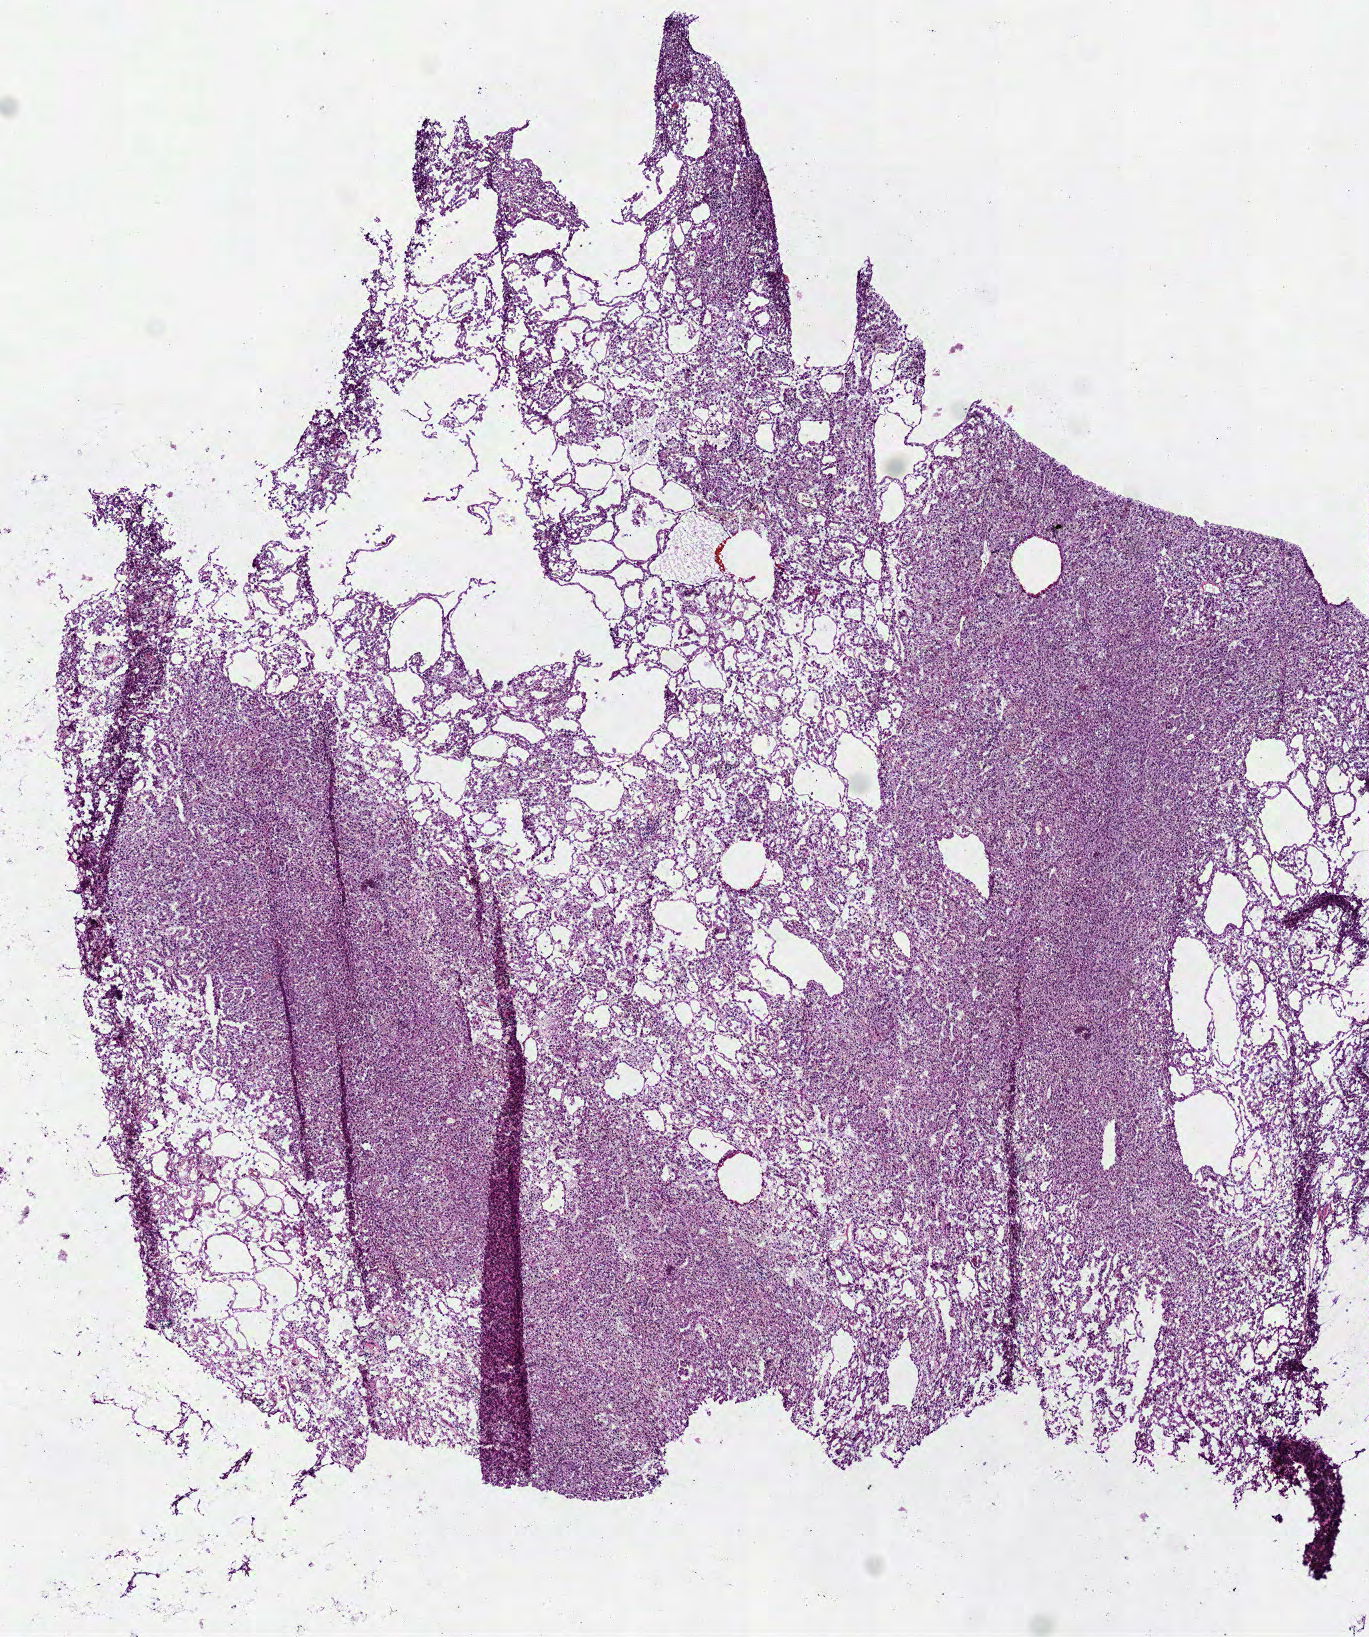
Whole-slide histology image, Hematoxylin and eosin (H&E) stained — whole scanned area (about 5.5 x 6.6 mm) shown as a low-resolution overview; frozen section from the bottom of the tissue portion; kidney, primary tumour sample. Female, age 61 years at initial diagnosis.
* AJCC pathologic stage: I (7th edition)
* pathologic diagnosis: Papillary adenocarcinoma, NOS